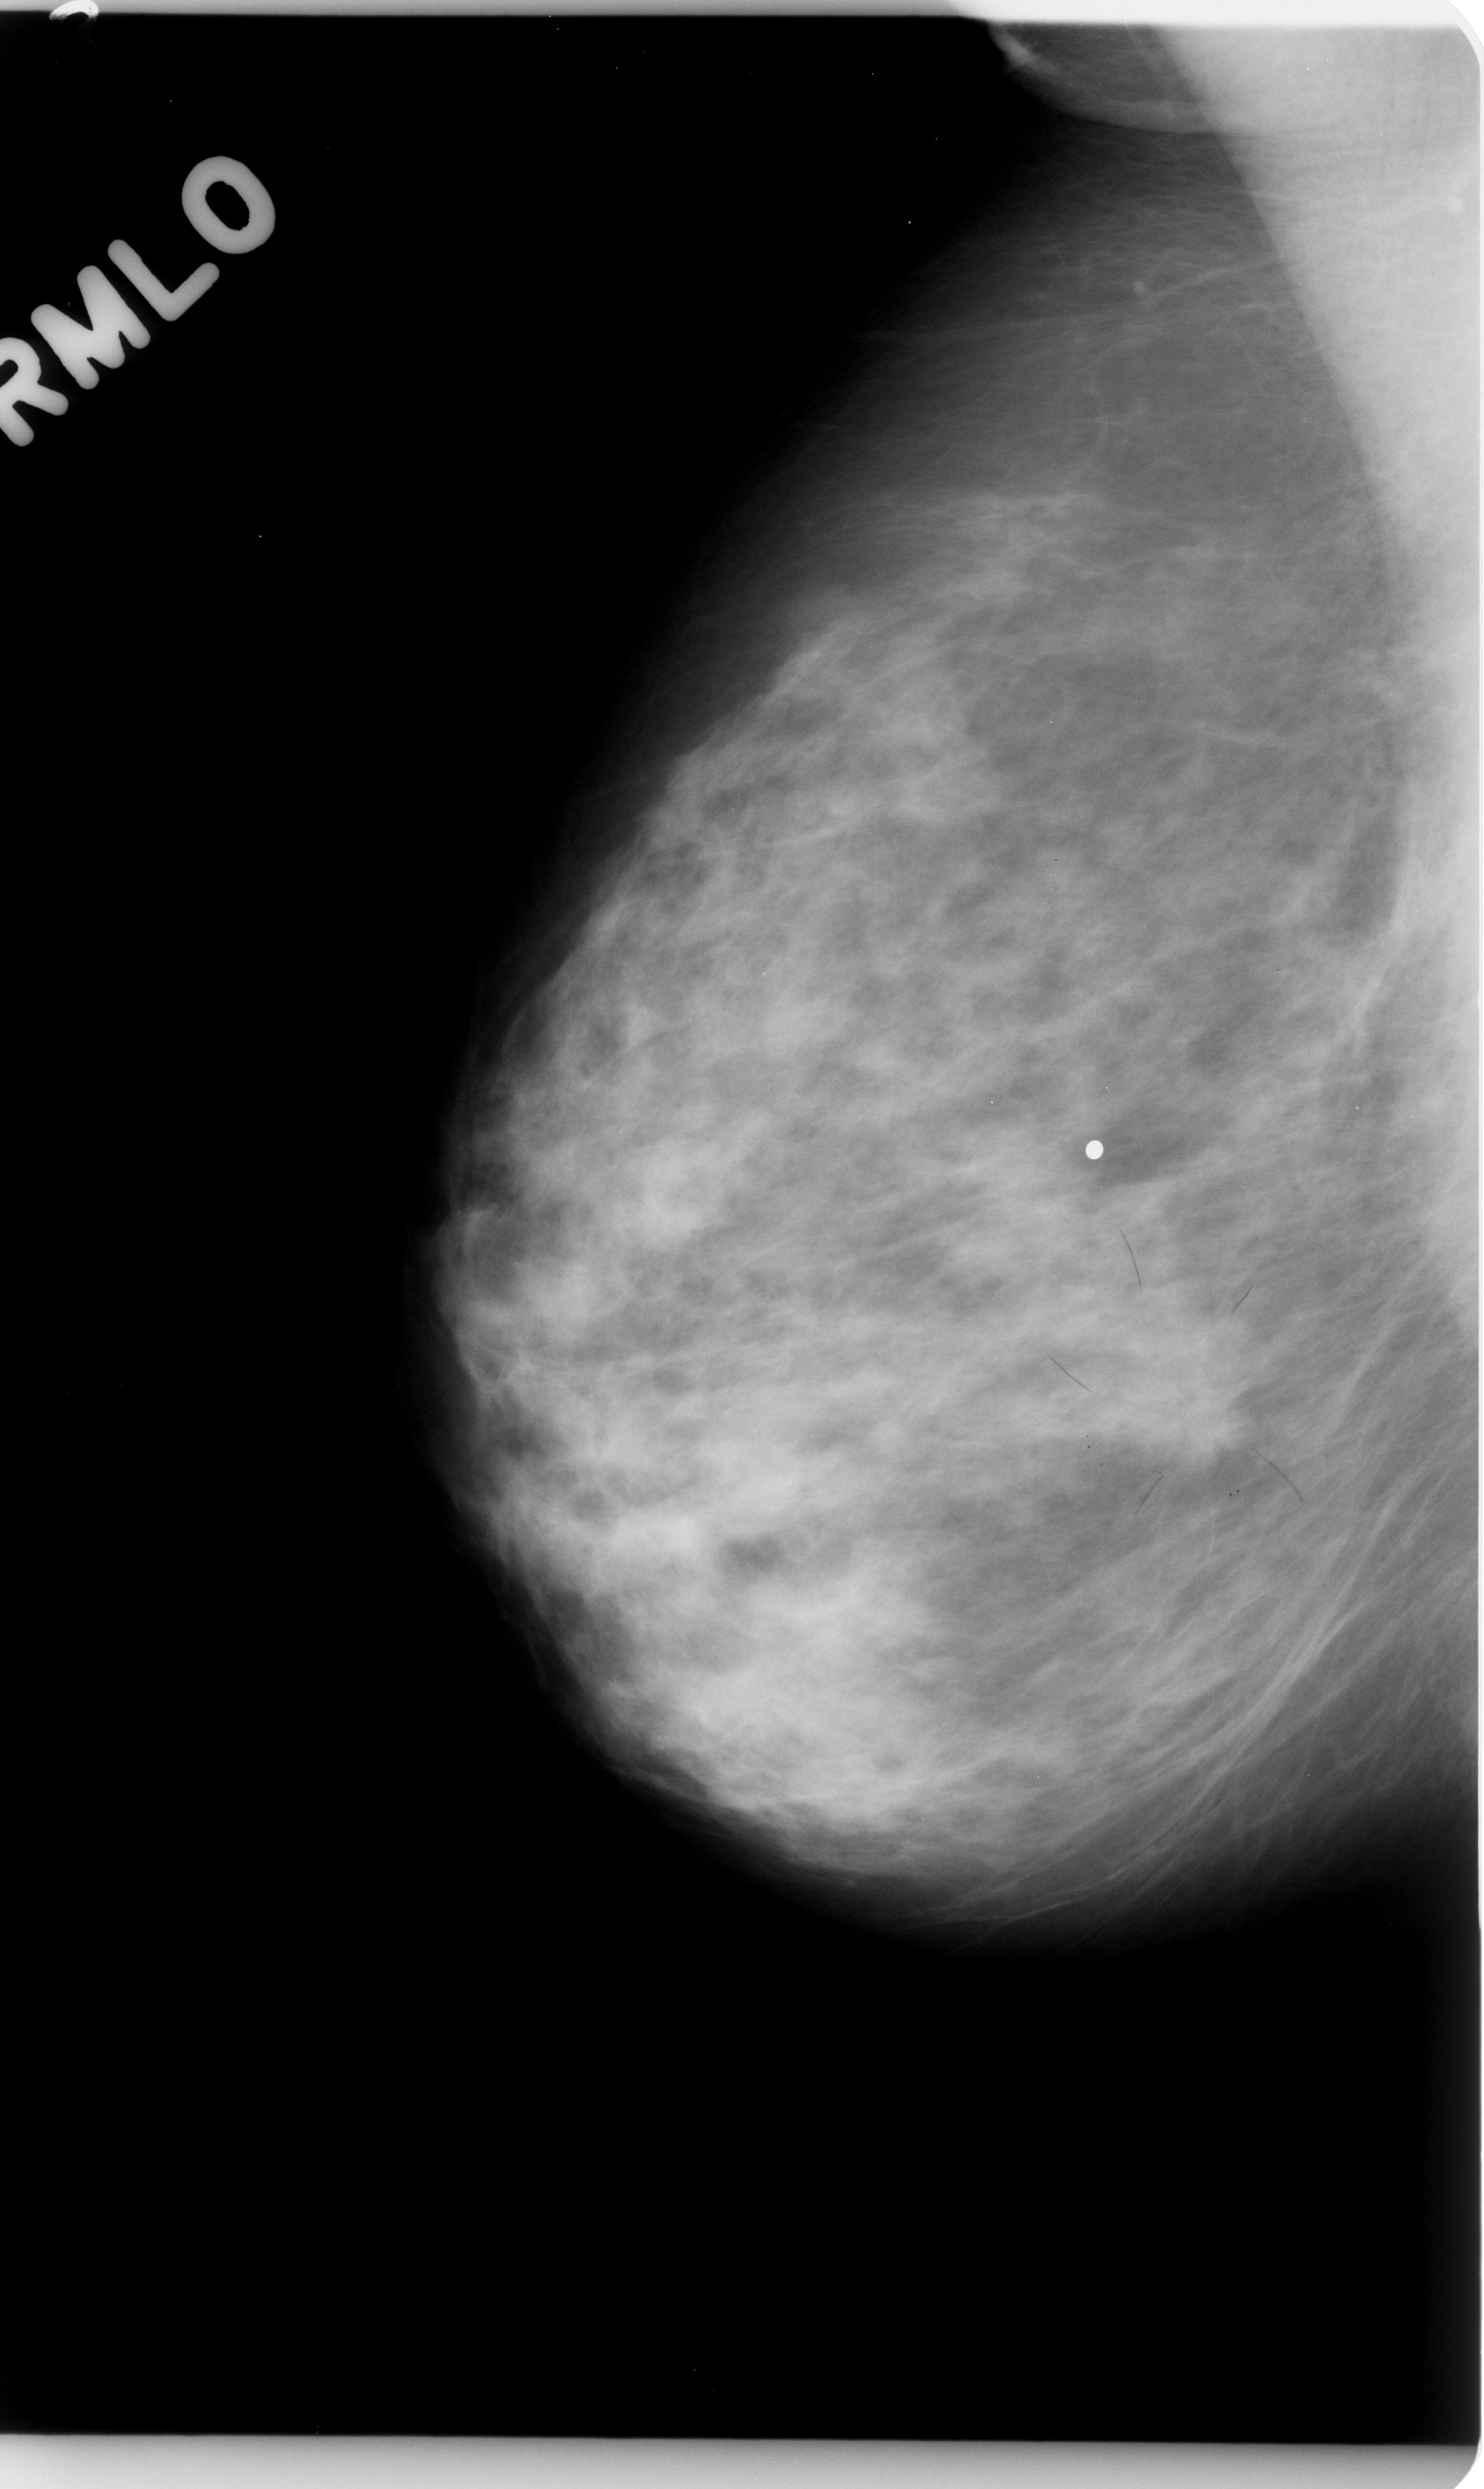
Mammogram (digitized film). Right breast. MLO view. Breast composition: scattered fibroglandular densities (BI-RADS density category 2 of 4). 1484 × 2489 image matrix.
Expert-marked regions of interest on this image (one box per marked abnormality):
- mass, shape irregular, margins spiculated; BI-RADS assessment category 4; pathology (as recorded): malignant: bounding box (x1, y1, x2, y2) in pixels: (1114, 1358, 1246, 1473)